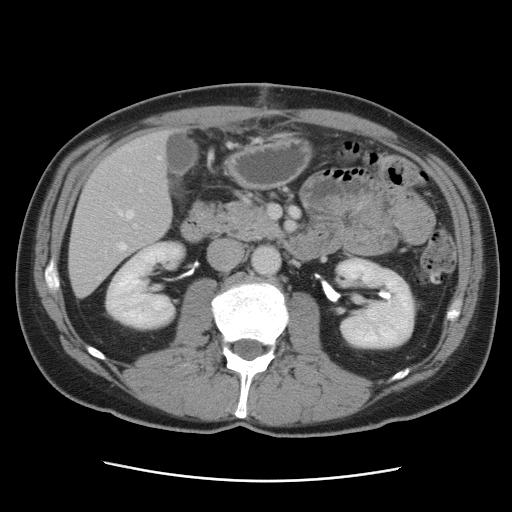
Contrast-enhanced abdominal CT, one axial slice. Slice 35 of 89 in the series (ordered by position). 120 kVp. Intravenous contrast given. Soft-tissue window (W 400 / L 40 HU). 512 × 512 image matrix, field of view 366 × 366 mm. Male patient, age 59 years. From the clinical record (not read from this slice): diagnosis: colorectal cancer liver metastases, imaged before liver resection; multiple liver metastases: yes.
Annotated regions visible in this slice (outlined manually by an expert reader):
- hepatic veins: bounding box (x1, y1, x2, y2) in pixels: (98, 157, 162, 279)
- liver: (69, 131, 172, 297)
- planned liver remnant (the part of the liver to remain after resection): (74, 130, 172, 245)
- portal vein (with intrahepatic branches): (135, 189, 142, 228)